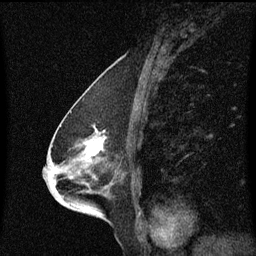
Breast MRI (dynamic contrast-enhanced), one sagittal slice; position 33 of 60 along the scan axis; dynamic contrast-enhanced series, image 2 of 3 at this slice position (ordered by acquisition); 1.5 T; TE 4.2 ms, TR 8.4 ms; 2 mm slice thickness; 256 × 256 image matrix, field of view 200 × 200 mm. Patient: female, 68 years. Case-level facts recorded for this patient, not image findings: setting: breast cancer imaged before/during neoadjuvant chemotherapy; receptor status: triple-negative.
Outlined on this slice (semi-automatically segmented with operator editing):
- analysis volume of interest (the breast-tissue region the enhancement analysis was run in; not a lesion): bounding box [x1, y1, x2, y2] px = [41, 114, 132, 203]
- tumour enhancement mask (voxels above the 70 % enhancement threshold inside the analysis volume of interest): [51, 140, 103, 175]